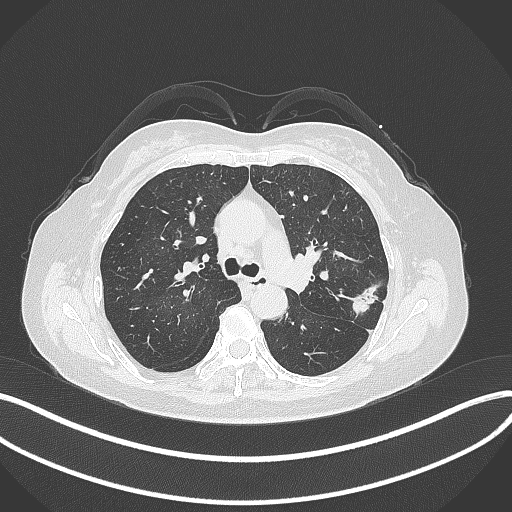
Chest CT, one axial slice. Slice 209 of 319 in the series (ordered by position). 120 kVp. Lung window (W 1500 / L -600 HU). 1 mm slice thickness. 512 × 512 image matrix. Patient: female, 60 years. From the clinical record (not read from this slice): clinical TNM (as recorded): T1c N0 M0.
Structures marked on this image (bounding box drawn by a radiologist):
- lung tumour (recorded histology: adenocarcinoma): bounding box (x1, y1, x2, y2) in pixels: (346, 278, 380, 319)